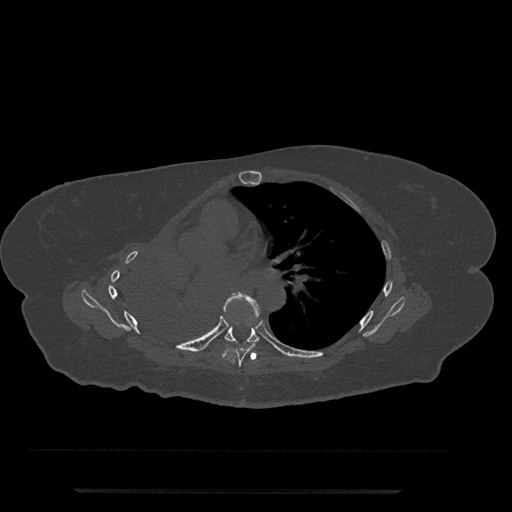
CT including the spine, one axial slice. Position 470 of 797 along the scan axis. Reconstruction kernel Br40s/3. Bone window (W 1800 / L 400 HU). 0.5 mm slice thickness. 512 × 512 image matrix. Patient: female, 51 years. From the clinical record (not read from this slice): primary cancer: neuro; vertebrae with lytic lesions (as recorded): T8.
Outlined on this slice (semi-automatically segmented with operator editing):
- T6 vertebra: box from (x=223, y=292) to (x=260, y=367) px
- T7 vertebra: (x=224, y=319)–(x=260, y=344)